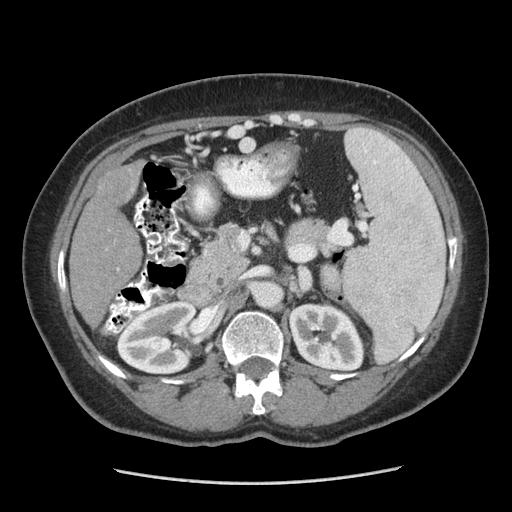
Contrast-enhanced abdominal CT (liver protocol), one axial slice. Position 137 of 185 along the scan axis. Reconstruction kernel STANDARD. 140 kVp. Soft-tissue window (W 400 / L 40 HU). 2.5 mm slice thickness. 512 × 512 image matrix. From the clinical record (not read from this slice): diagnosis: hepatocellular carcinoma (patient treated with transarterial chemoembolisation; whether this scan precedes or follows treatment is not stated here); TNM stage (as recorded): Stage-I; Child-Pugh class: A; tumour differentiation: poorly differentiated; tumour nodularity: uninodular.
Outlined on this slice (semi-automatically segmented with operator editing):
- liver parenchyma outside the tumour (the mass and vessels are separate outlines, so this box may not span the whole liver): bounding box (x1, y1, x2, y2) in pixels: (70, 164, 142, 325)
- mass: (99, 159, 138, 206)